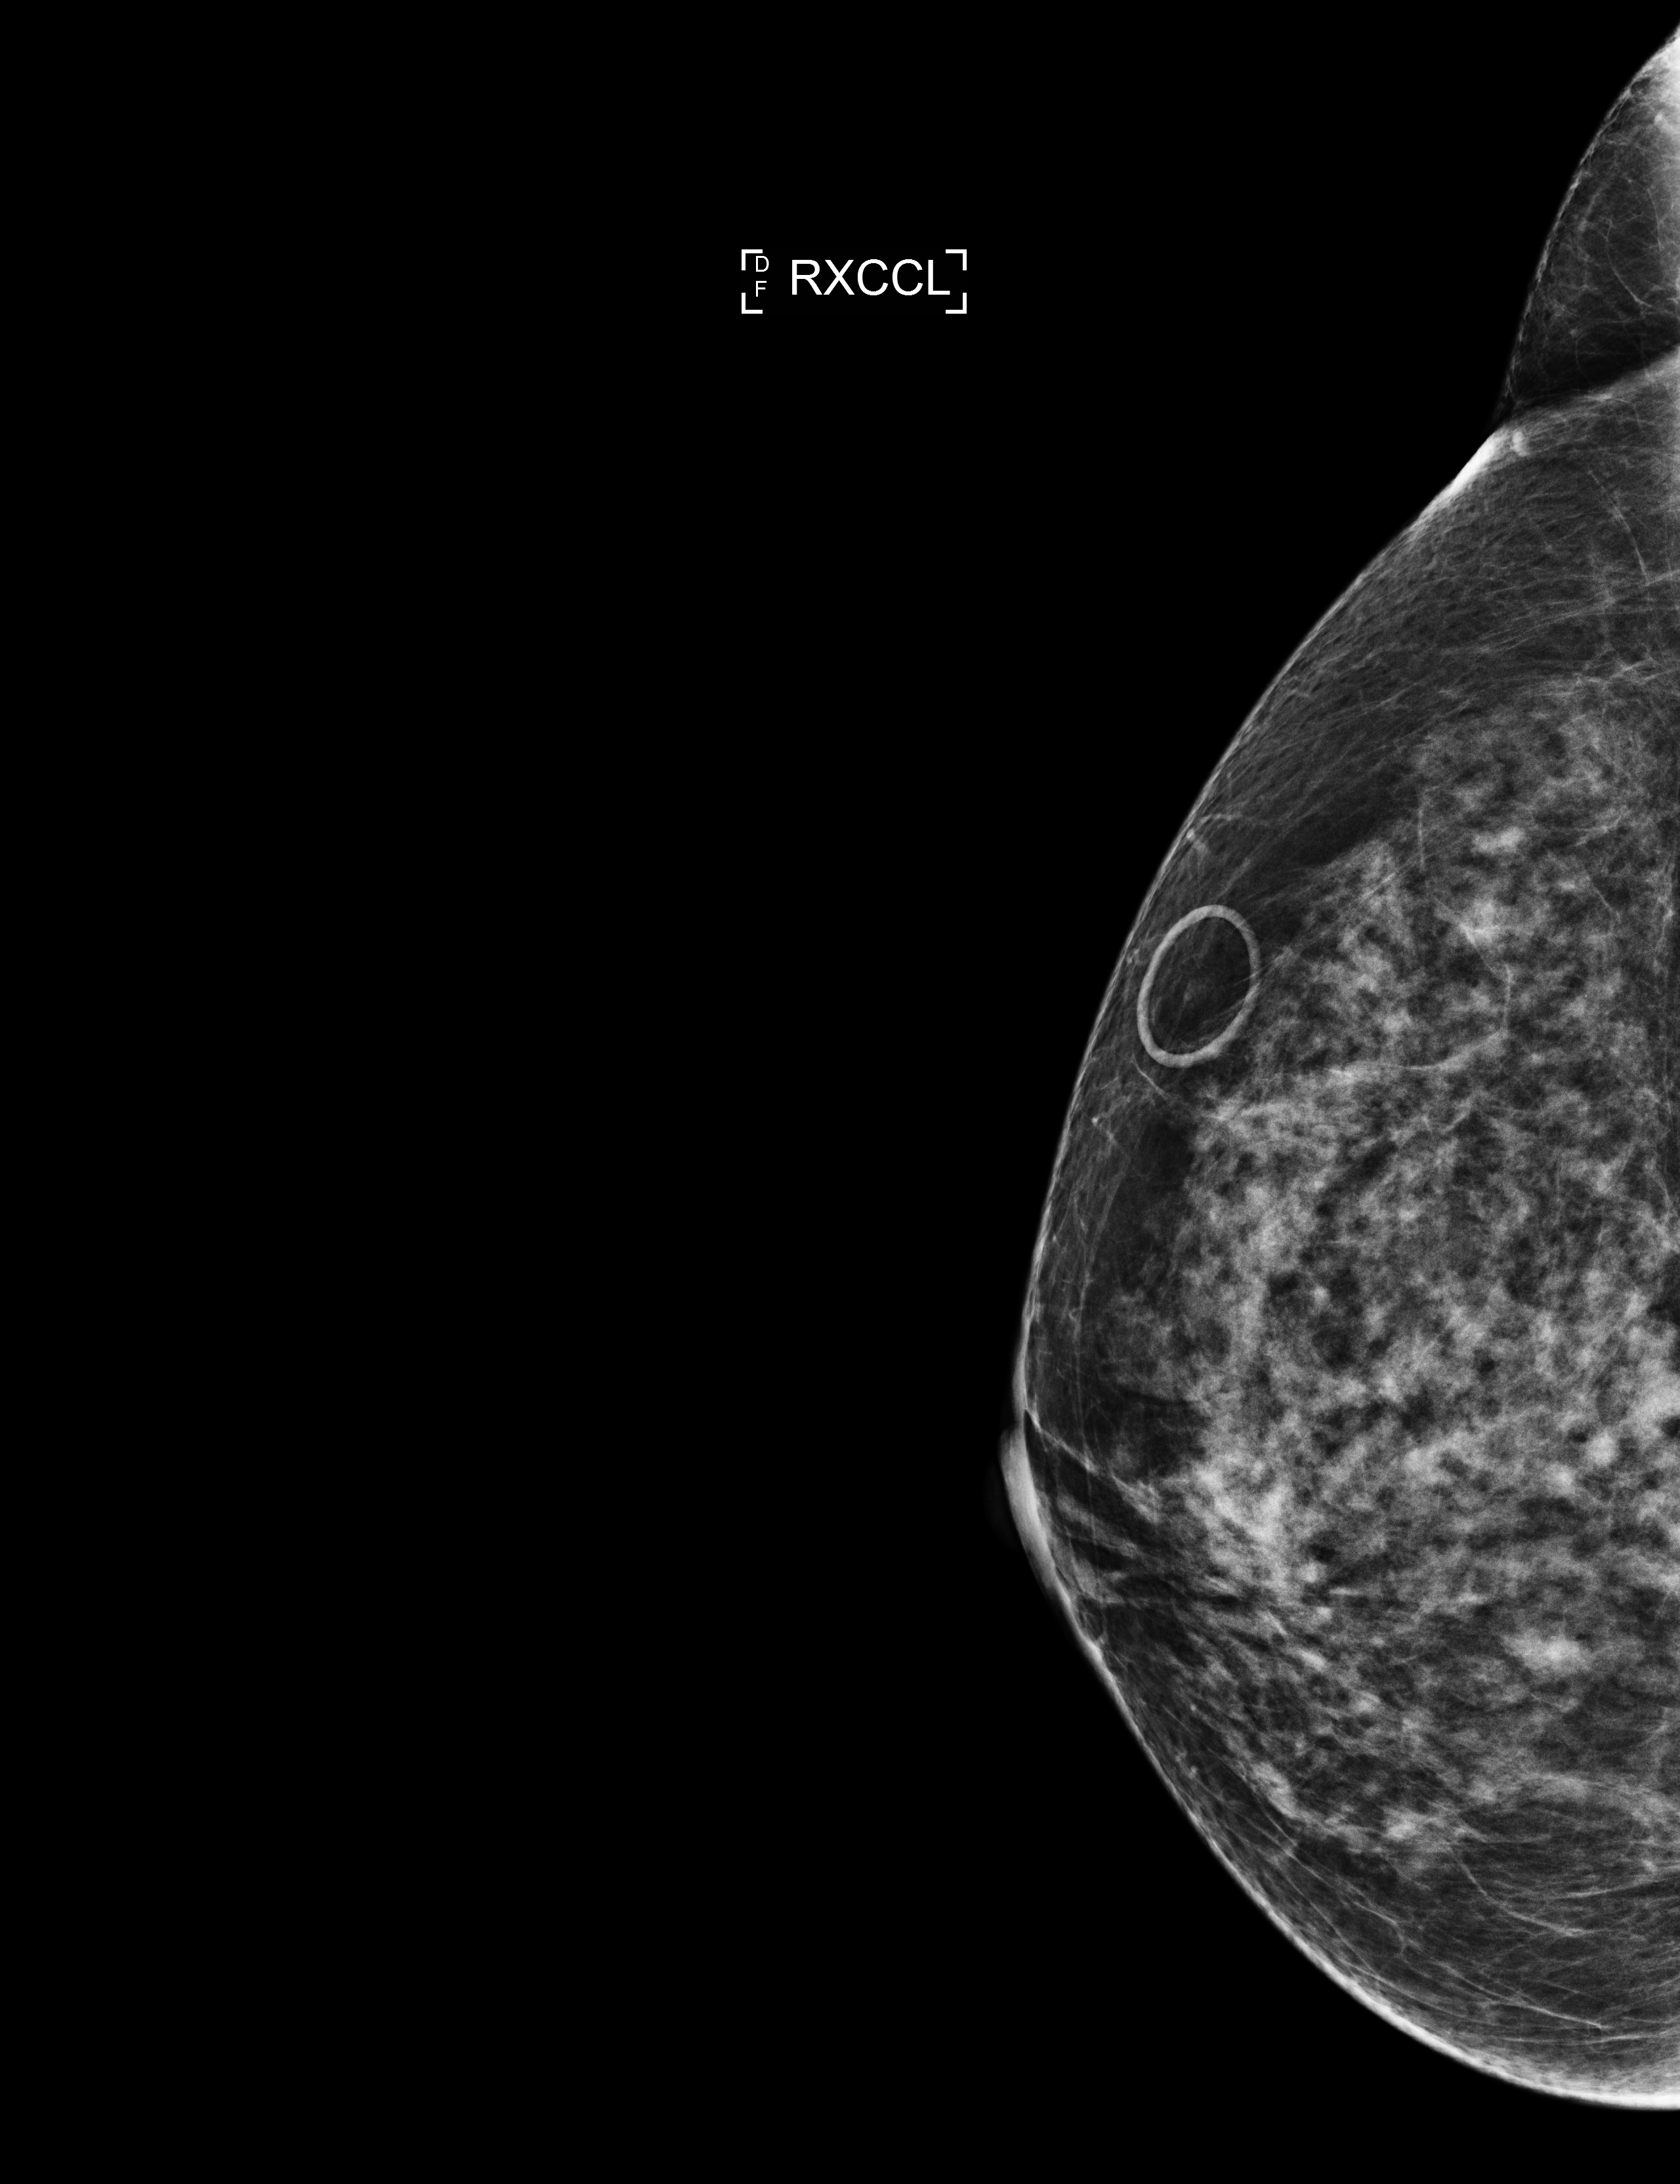
Full-field digital mammogram (FFDM); right breast; laterally exaggerated craniocaudal (XCCL) view; annual screening mammography examination; compressed breast thickness 65 mm. Patient: female, 65 years.
Breast density at the screening exam (both breasts): heterogeneously dense (BI-RADS density category c). Final BI-RADS assessment for this screening round (tomosynthesis exam, both breasts): category 1. Recall: no recall after this screen.